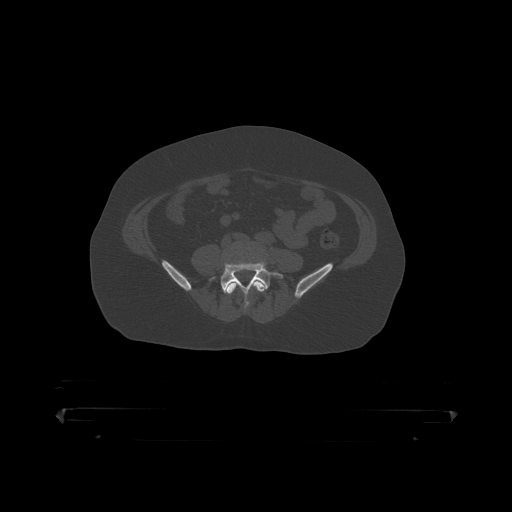
CT including the spine, one axial slice; slice 48 of 390 in the series (ordered by position); reconstruction kernel STANDARD; 120 kVp; bone window (W 1800 / L 400 HU); 512 × 512 image matrix, field of view 650 × 650 mm. Patient: male, 60 years. From the clinical record (not read from this slice): primary cancer: prostate.
Outlined on this slice (semi-automatic segmentation, software-assisted and operator-edited):
- L4 vertebra: box from (x=226, y=280) to (x=265, y=309) px
- L5 vertebra: (x=221, y=264)–(x=283, y=295)